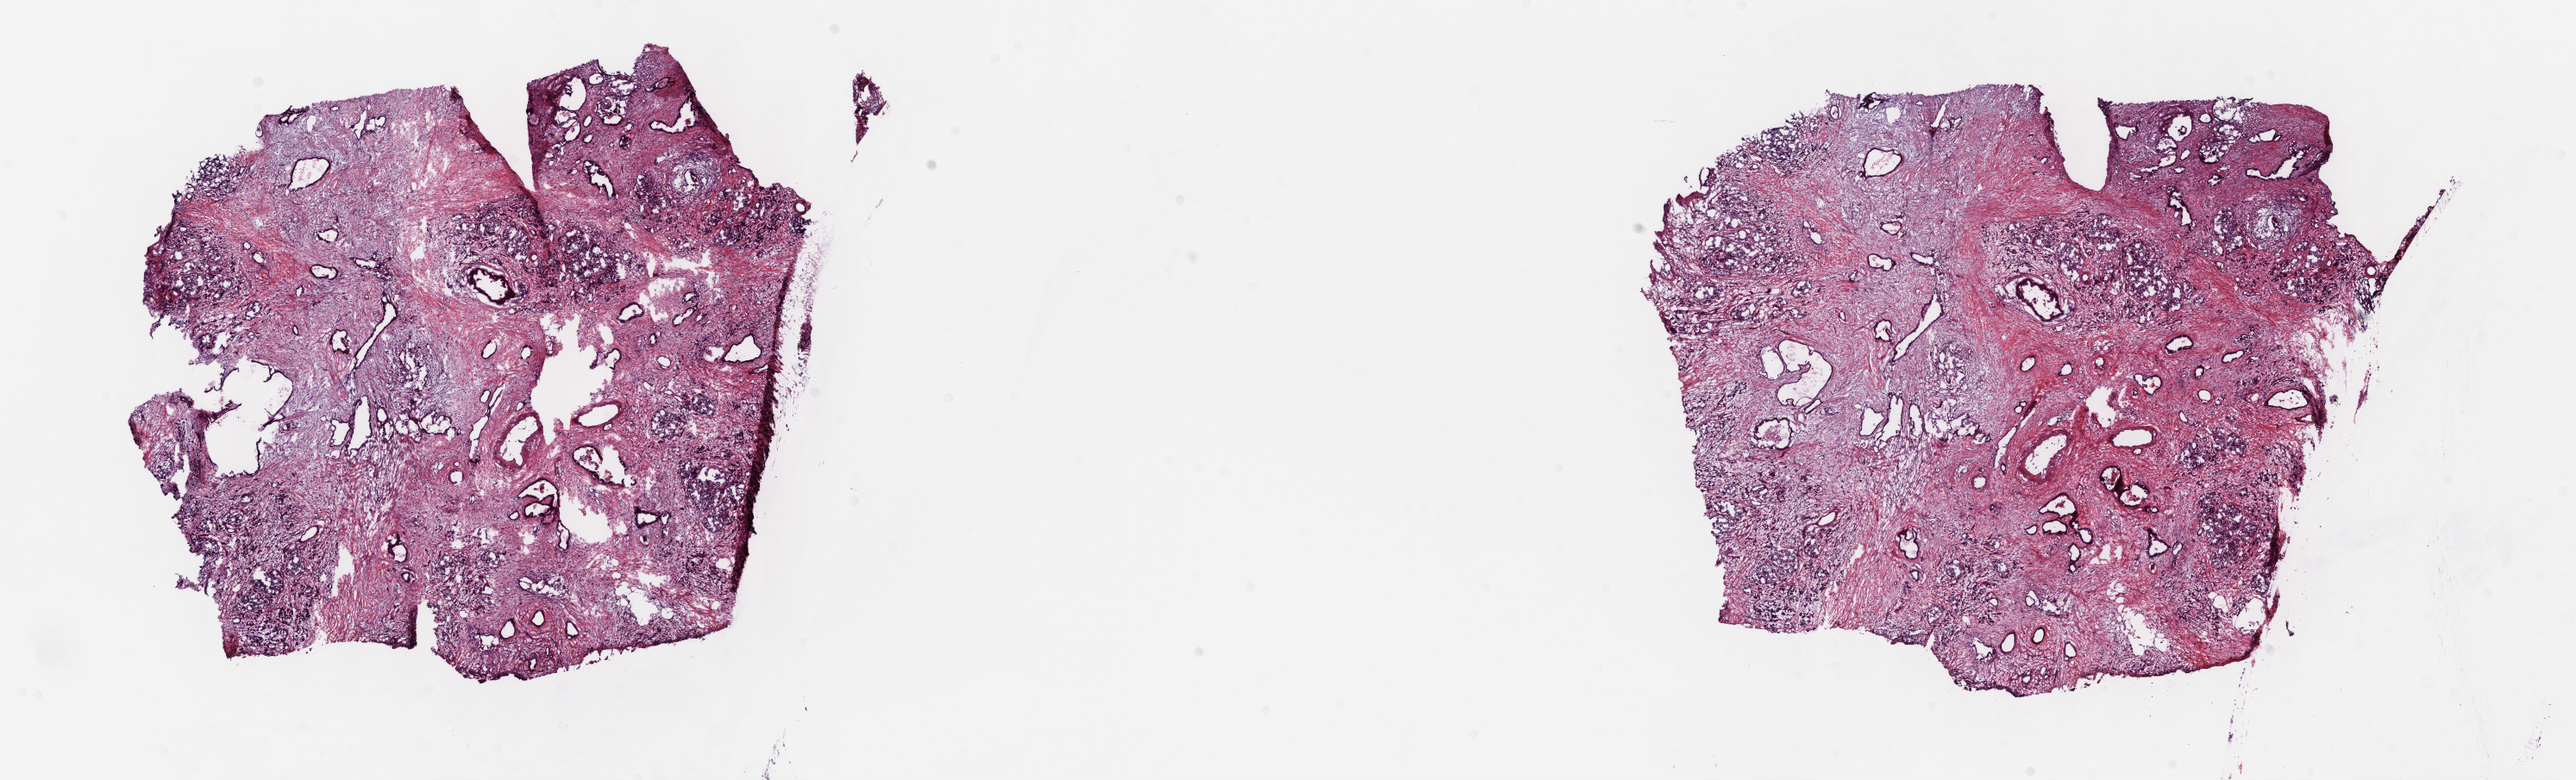
Digitized Hematoxylin and eosin (H&E) stained tissue section (whole slide), whole scanned area (about 24.2 x 7.3 mm, acquisition: 40x scan) shown as a low-resolution overview; frozen section from the top of the tissue portion; pancreas, primary tumour sample. Male, age 71 years at initial diagnosis. Slide review estimates, as recorded: tumour cells 100%, tumour nuclei 60%.
Pathologic diagnosis: Infiltrating duct carcinoma, NOS (head of pancreas).